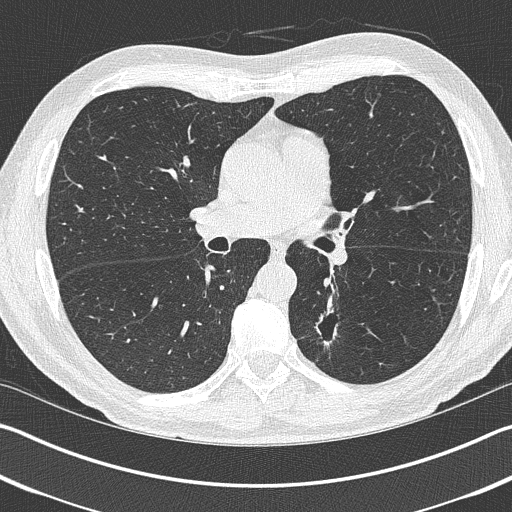
Low-dose screening chest CT, axial slice, baseline screening round, lung window (W 1500 / L -600 HU), slice 168 of 402 in the series, 512 × 512 image matrix. Male, age 69 years at enrolment.
- Expert reader's lesion annotation, bounding box [x1, y1, x2, y2] px = [297, 306, 353, 361].
- Screening reader's record for this exam (one nodule recorded; not confirmed to be the boxed lesion): non-calcified nodule or mass ≥4 mm, left upper lobe, 19 × 19 mm, spiculated (stellate) margins, pre-existing on the prior screen: yes.
- Official screen result: positive, change unspecified: nodule(s) >= 4 mm or enlarging nodule(s), mass(es), or other non-specific abnormalities suspicious for lung cancer.
- Later outcome: lung cancer diagnosed 202 days after this screen — non-small cell carcinoma, left lower lobe, stage IIIA (AJCC 6th edition), 20 mm at pathology.